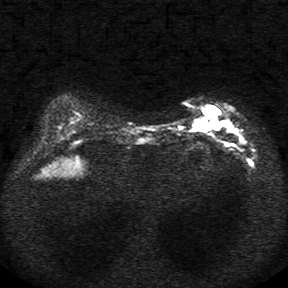
Breast MRI, one axial slice; position 9 of 34 along the scan axis; diffusion-weighted series; image 2 of 4 stored at this slice position (different b-values; order by instance number); 1.5 T; 5 mm slice thickness; 288 × 288 image matrix. Female patient.
Structures marked on this image (expert manual segmentation):
- tumour on diffusion-weighted imaging: box from (x=192, y=106) to (x=233, y=132) px